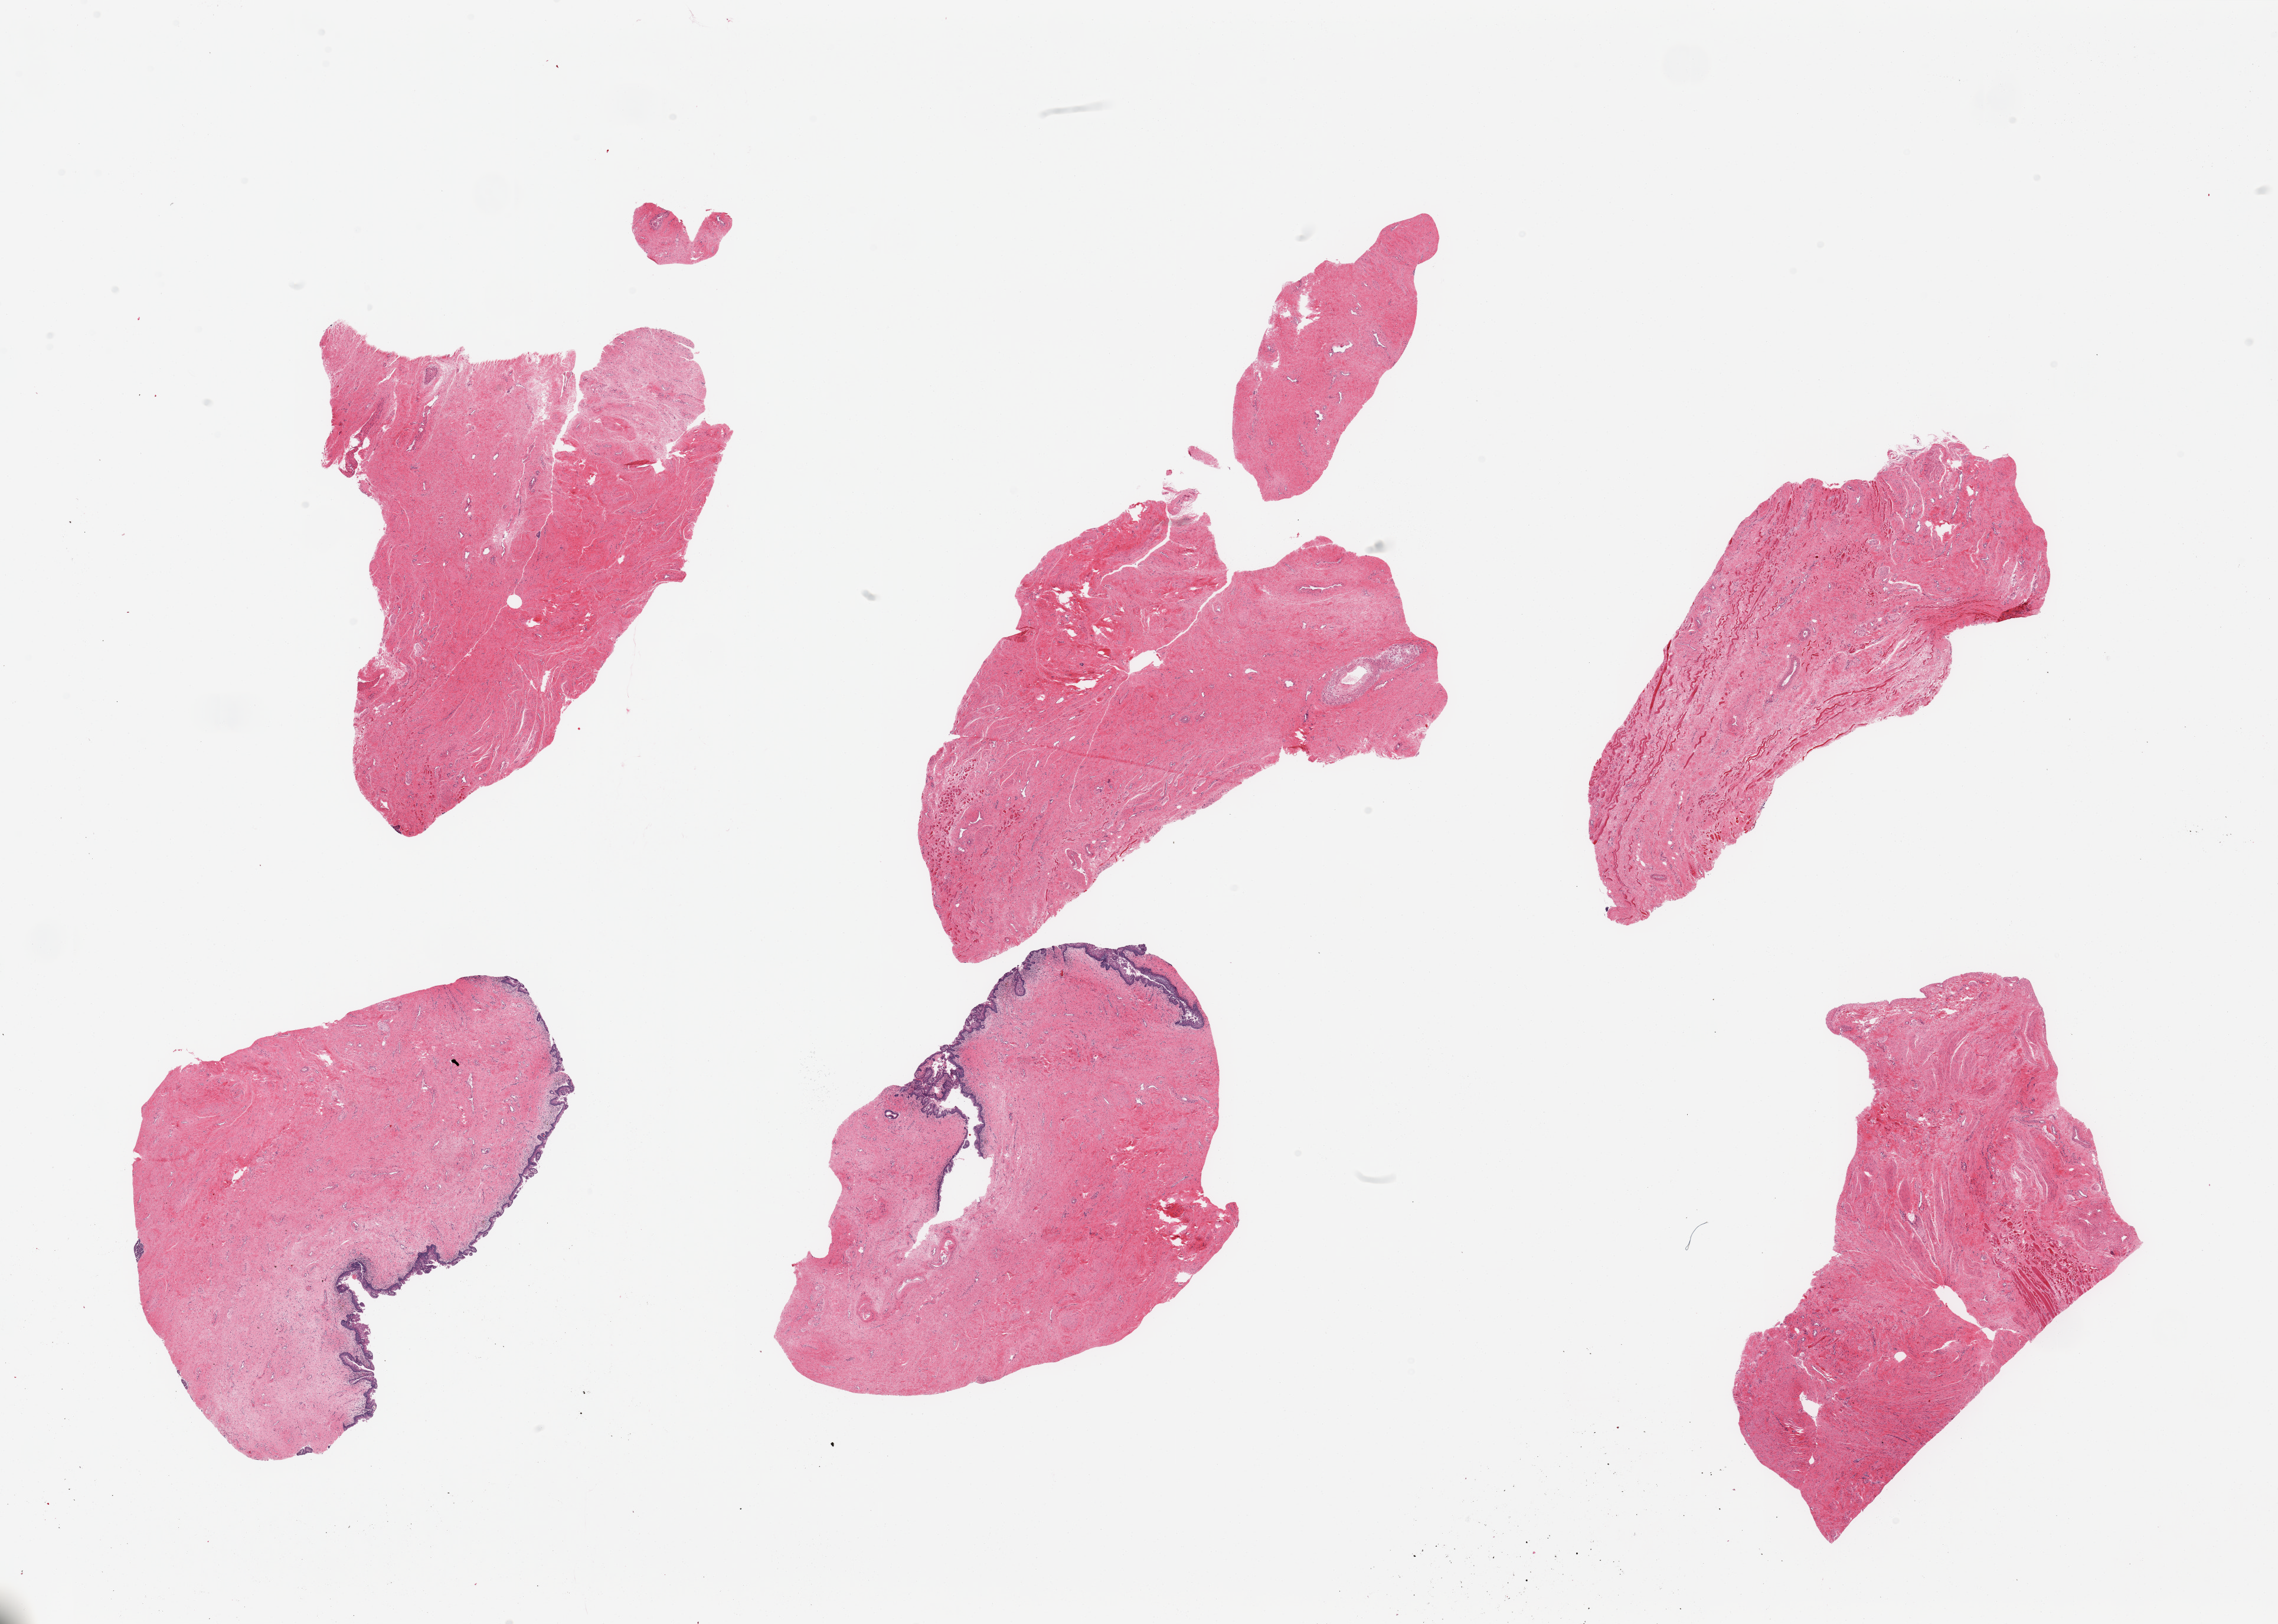
Whole-slide image, hematoxylin and eosin (H&E) stain — whole scanned area (about 30.5 x 21.8 mm, acquisition: 20x scan) shown as a low-resolution overview, PAXgene-fixed paraffin-embedded (PFPE) section, section of vagina (target tissue), tissue donor sample. Donor: female.
Reviewer comment on this tissue sample: 6 pieces (fragmented); mostly stroma with skeletal muscle, only 2 pieces include partially denuded epithelium.